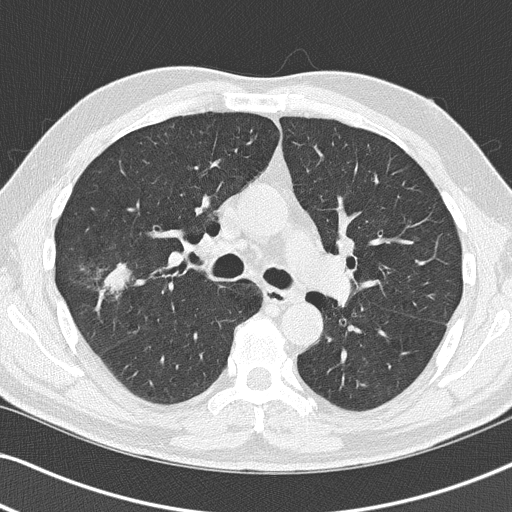
Axial slice from a low-dose chest CT screening exam, first (baseline) screen, lung window (W 1500 / L -600 HU), lung (sharp) reconstruction kernel (B50f), slice 61 of 140 in the series. Male, age 67 years at enrolment. Former smoker at enrolment.
Lesion marked by an expert reader, bounding box (x1, y1, x2, y2) in pixels: (70, 252, 145, 319). Screening reader's record for this exam (one nodule recorded; not confirmed to be the boxed lesion): non-calcified nodule or mass ≥4 mm, right upper lobe, 26 × 24 mm, spiculated (stellate) margins, soft tissue attenuation. Later outcome: lung cancer diagnosed 49 days after this screen — squamous cell carcinoma, NOS, right upper lobe, poorly differentiated (G3), stage IA (AJCC 6th edition), 27 mm at pathology.